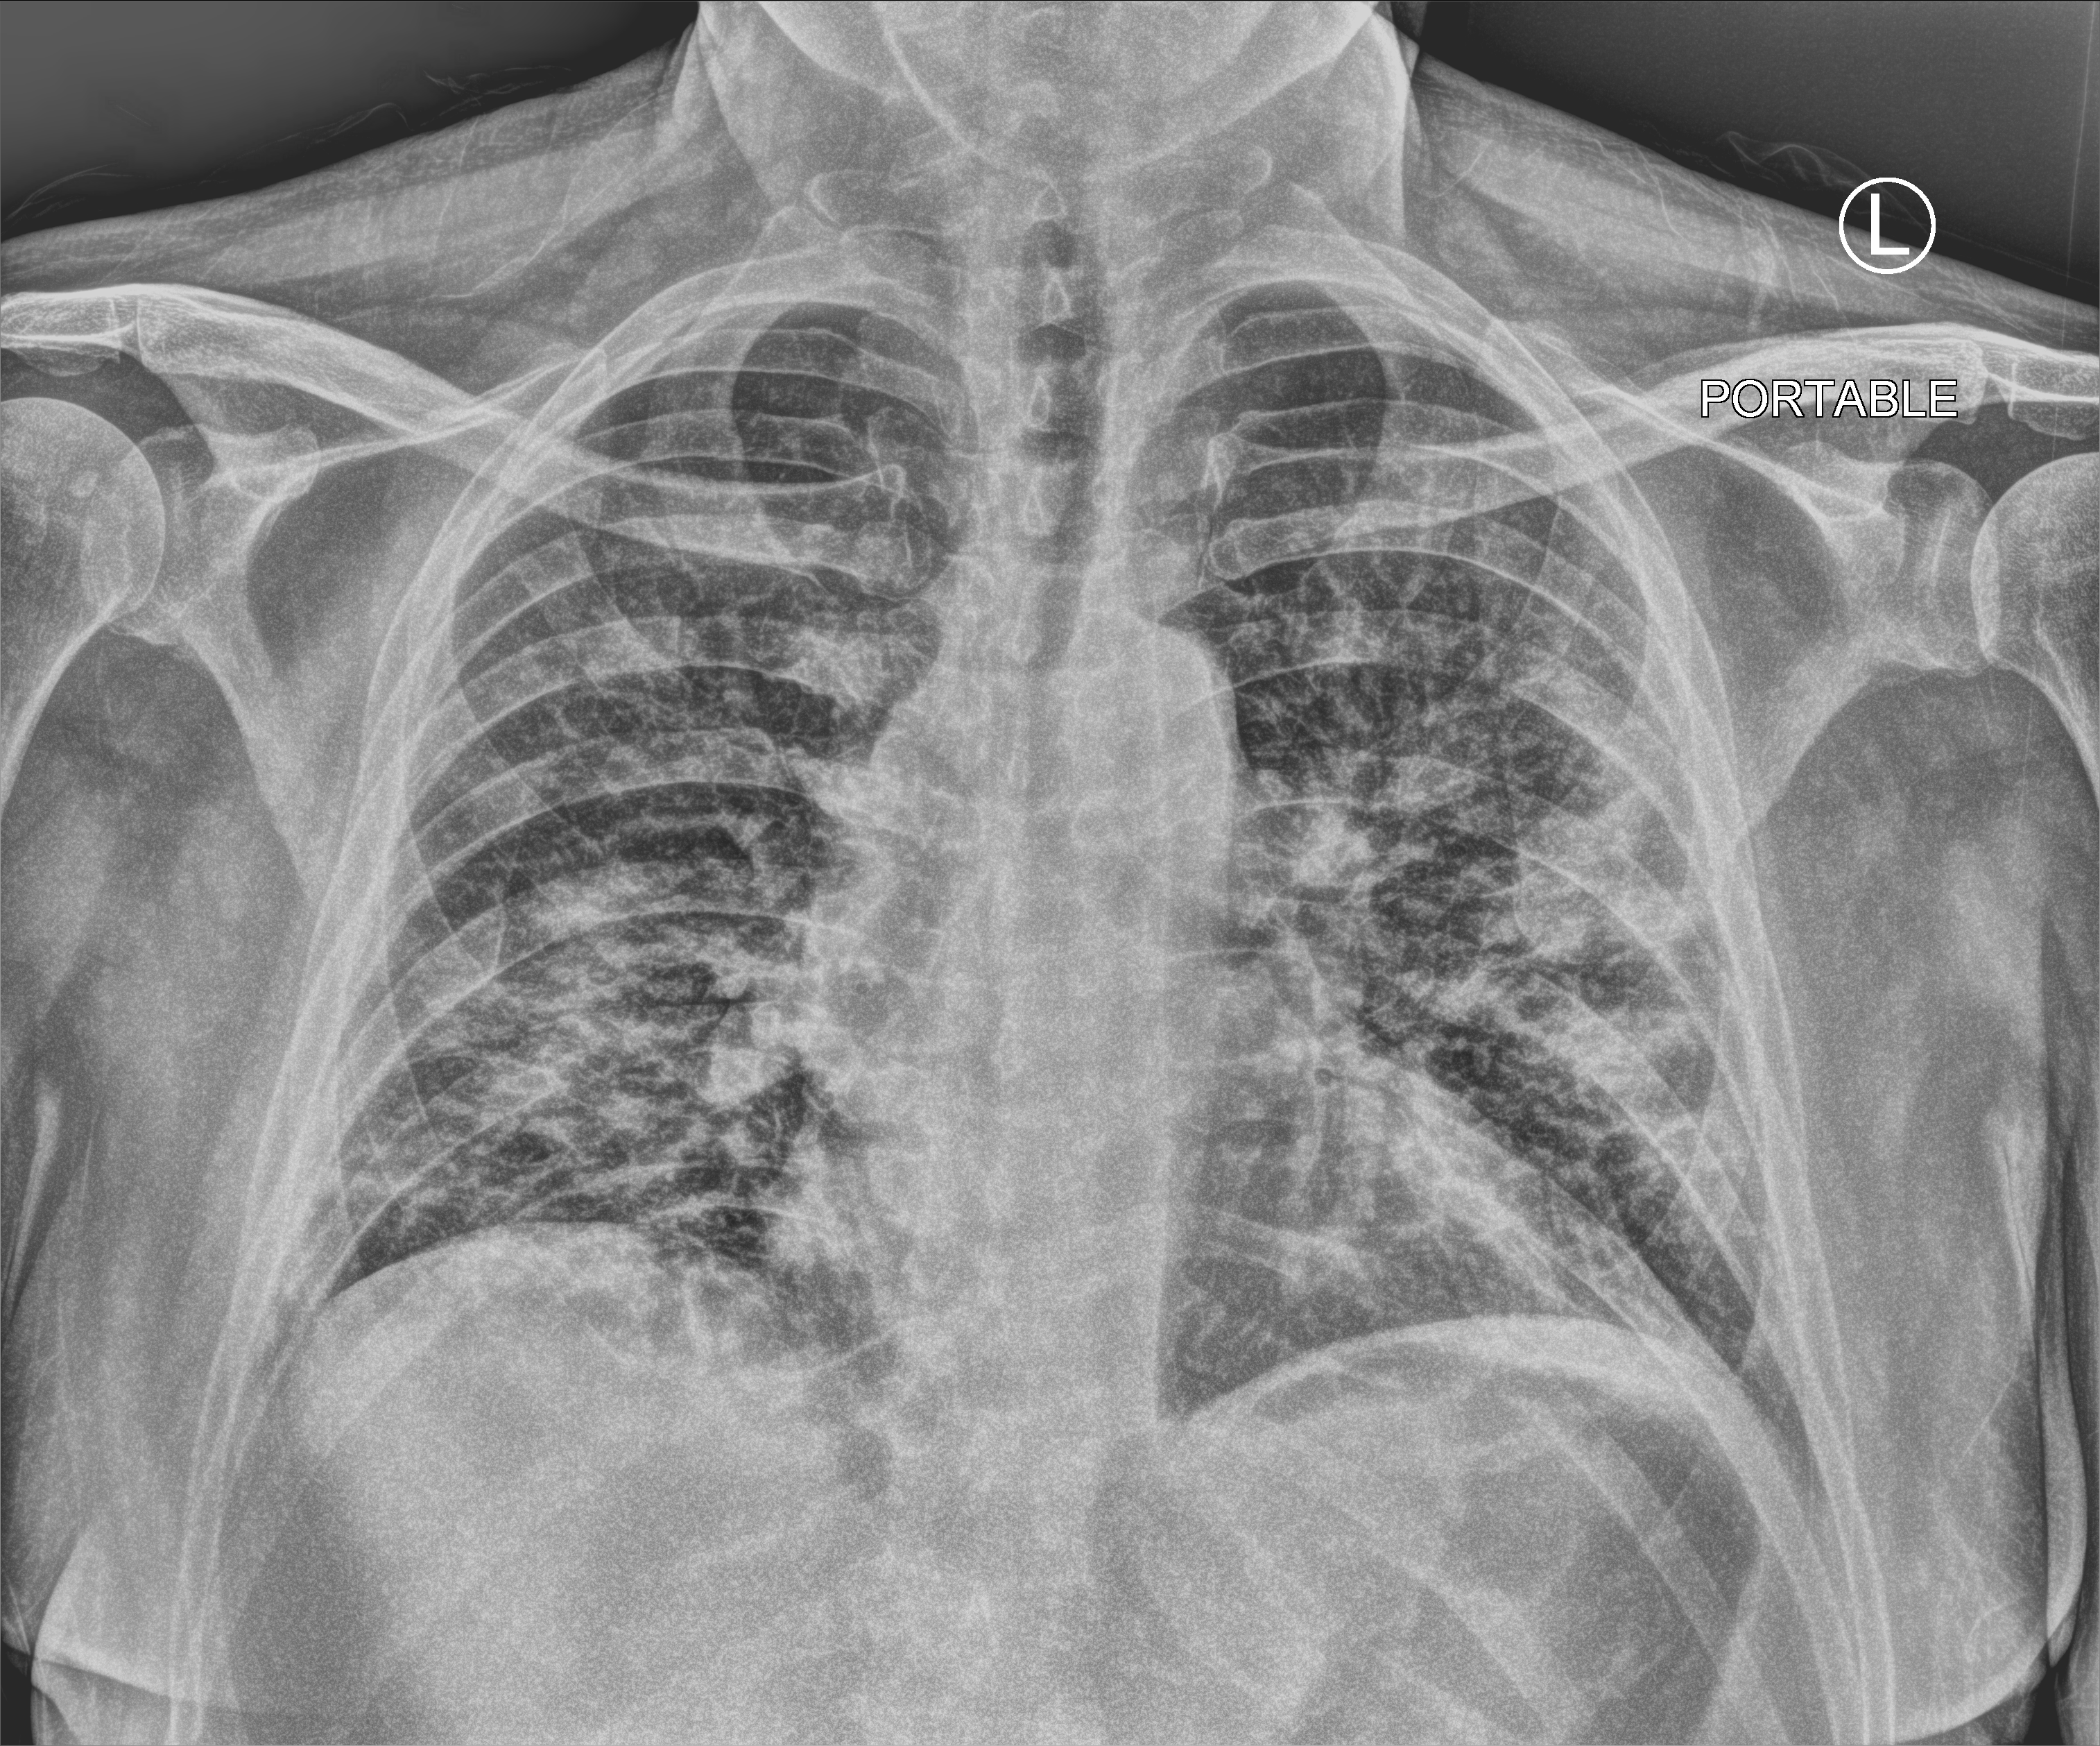
Chest X-ray (portable). Patient hospitalised with COVID-19; male, aged 18–59 years.
From the hospital-stay record, not from the radiograph (when in the stay this image was taken is not recorded):
- length of hospital stay: 1 day